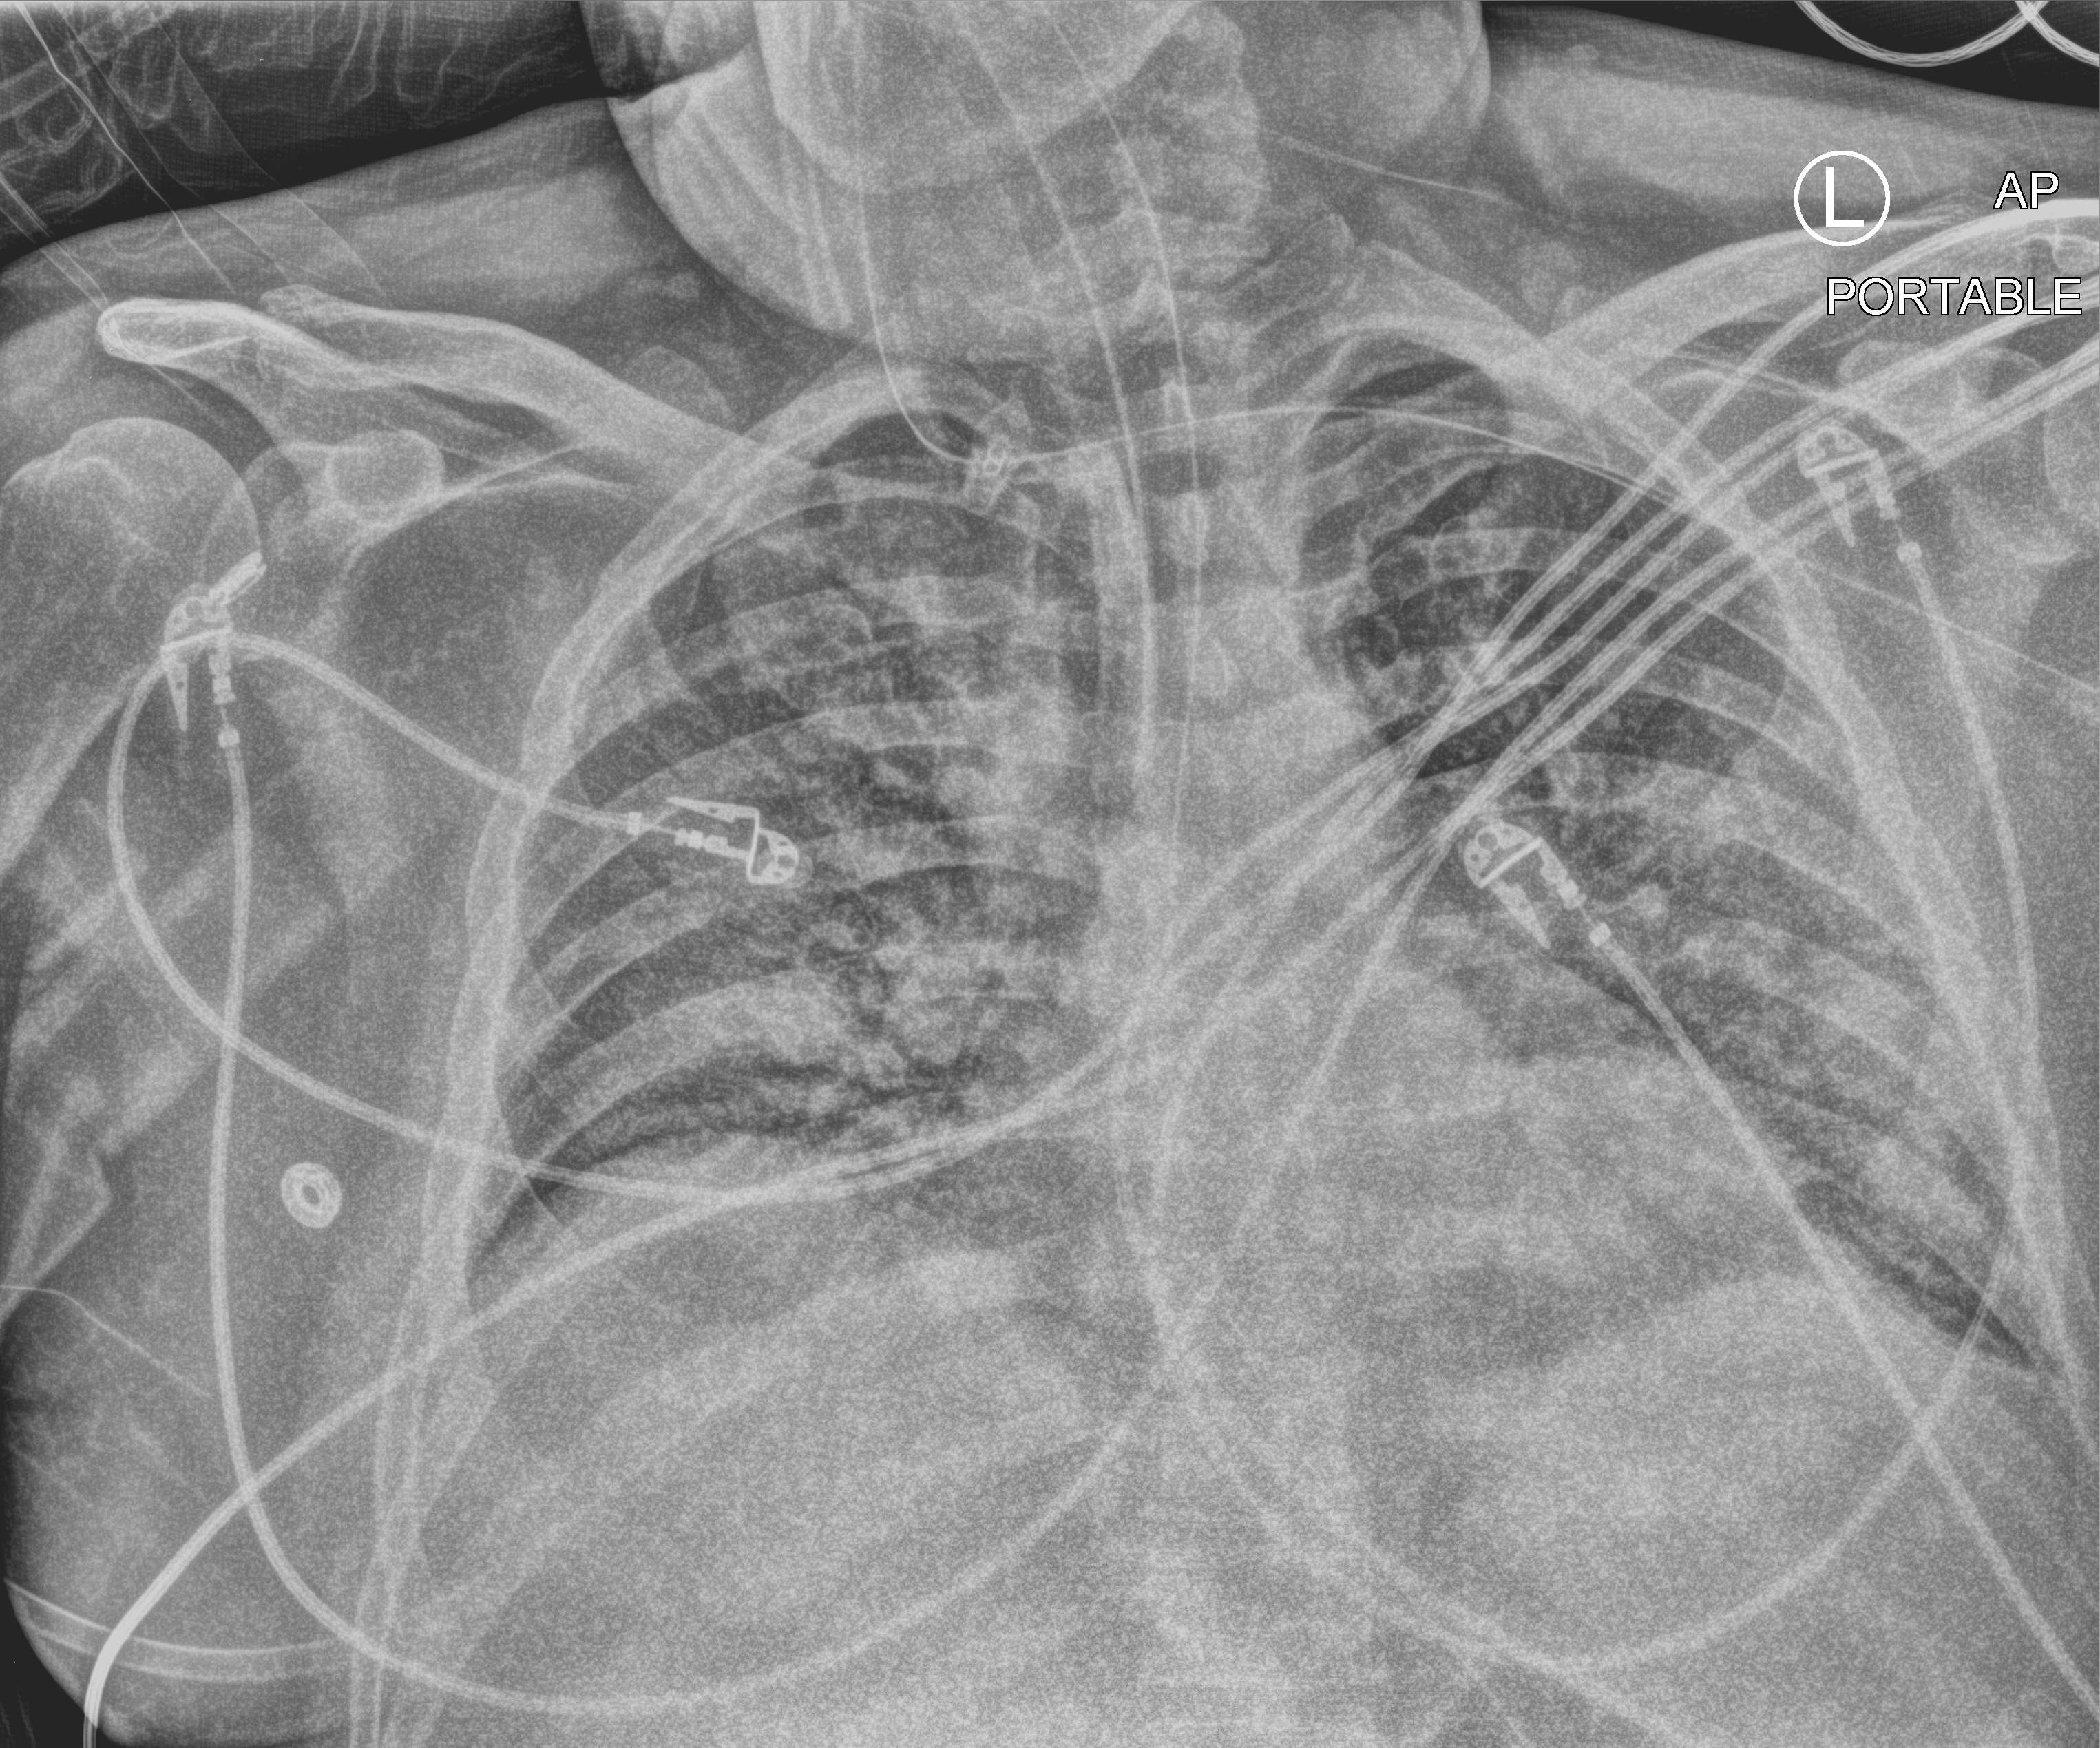
Portable chest radiograph, anteroposterior (AP) projection. Patient hospitalised with COVID-19; male, aged 18–59 years.
From the hospital-stay record, not from the radiograph (when in the stay this image was taken is not recorded): length of hospital stay: 80 days; admitted to intensive care during this hospital stay: yes; mechanically ventilated during this hospital stay: yes.